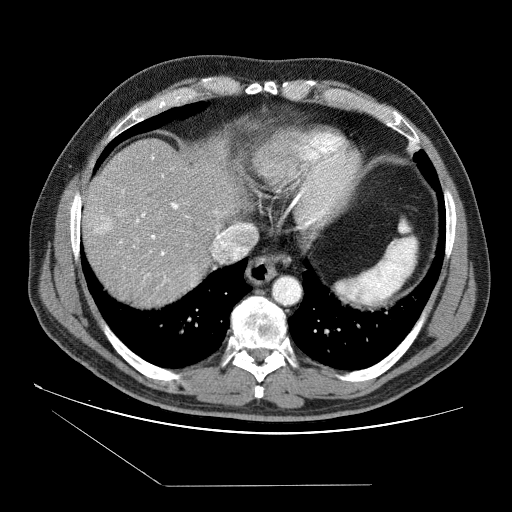
Contrast-enhanced abdominal CT (liver protocol), one axial slice; position 72 of 87 along the scan axis; soft-tissue window (W 400 / L 40 HU); 512 × 512 image matrix, field of view 400 × 400 mm. From the clinical record (not read from this slice): diagnosis: hepatocellular carcinoma (patient treated with transarterial chemoembolisation; whether this scan precedes or follows treatment is not stated here); TNM stage (as recorded): Stage-II; Child-Pugh class: B; tumour differentiation: no biopsy; tumour nodularity: multinodular.
Annotated regions visible in this slice (semi-automatic segmentation, software-assisted and operator-edited):
- abdominal aorta: box from (x=273, y=276) to (x=300, y=303) px
- liver parenchyma outside the tumour (the mass and vessels are separate outlines, so this box may not span the whole liver): (x=82, y=138)–(x=246, y=304)
- mass: (x=95, y=218)–(x=200, y=284)
- liver vessels: (x=101, y=157)–(x=217, y=282)